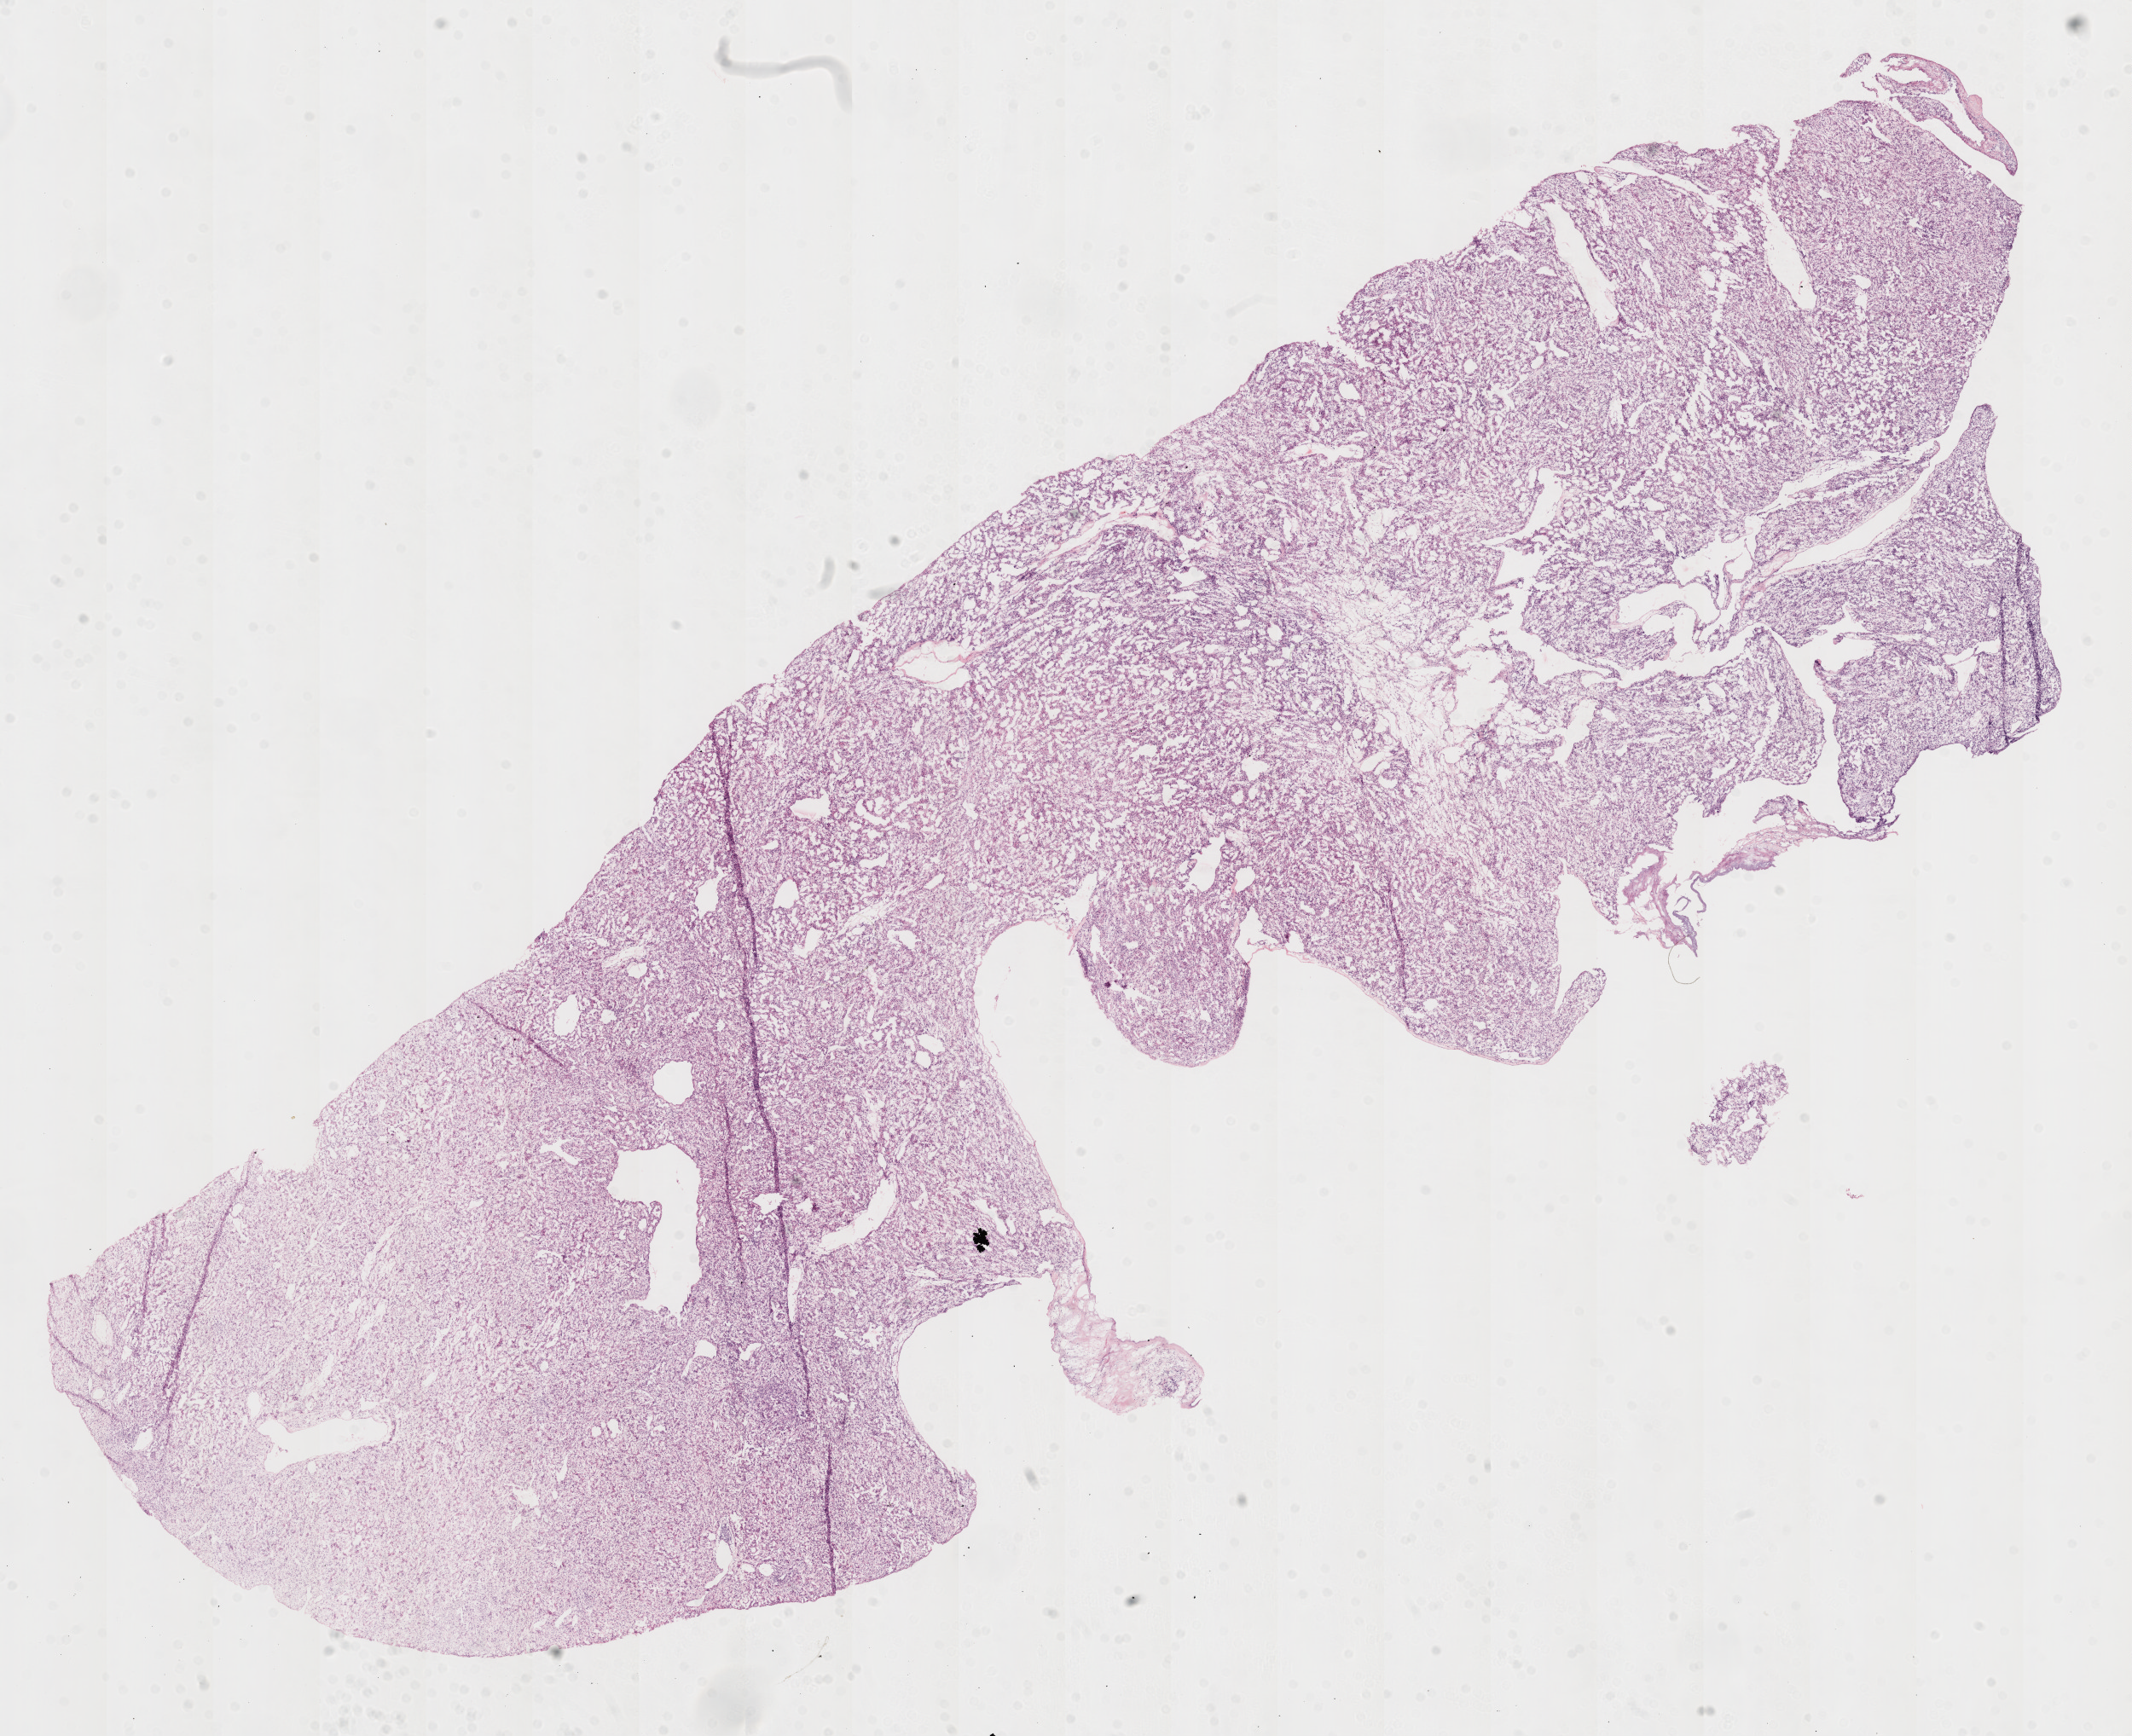
Digitized H&E-stained tissue section (whole slide), low-resolution overview of the scanned area, about 20.1 x 16.3 mm (slide scanned at 20x); frozen section from the top of the tissue portion; kidney, primary tumour sample. Male patient; age at initial diagnosis 82 years.
Diagnosis: Clear cell adenocarcinoma, NOS.